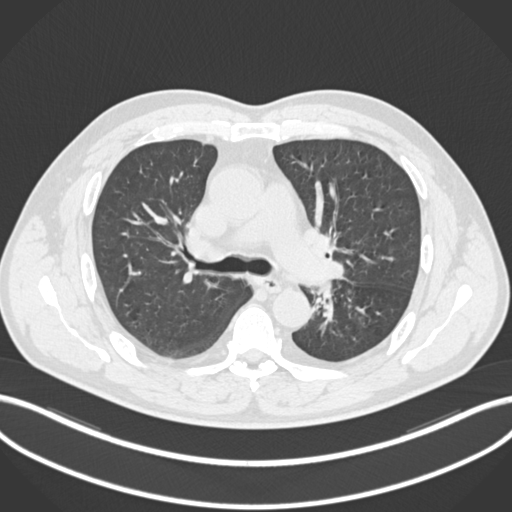
Chest CT, one axial slice. Position 145 of 223 along the scan axis. Reconstruction kernel B30f. 120 kVp. Lung window (W 1500 / L -600 HU). 1 mm slice thickness. 512 × 512 image matrix, field of view 400 × 400 mm. Male patient, age 50 years. From the clinical record (not read from this slice): clinical TNM (as recorded): T2a N3 M0.
Annotated regions visible in this slice (rectangle marked by the reading radiologist):
- lung tumour (recorded histology: squamous cell carcinoma): bounding box (x1, y1, x2, y2) in pixels: (310, 285, 335, 322)